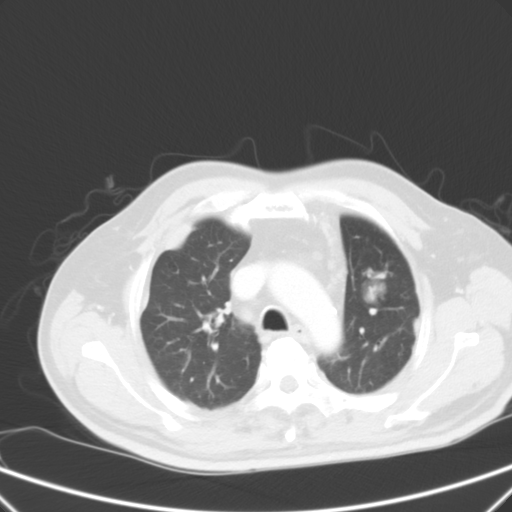
Chest CT, one axial slice. Position 44 of 59 along the scan axis. 120 kVp. Intravenous contrast given. Lung window (W 1500 / L -600 HU). 5 mm slice thickness. 512 × 512 image matrix, field of view 357 × 357 mm. Male patient, age 66 years. Case-level facts recorded for this patient, not image findings: clinical TNM (as recorded): T1c N3 M1a.
Structures marked on this image (rectangle marked by the reading radiologist):
- lung tumour (recorded histology: squamous cell carcinoma): bounding box <358,263,392,307> (left, top, right, bottom; pixels)